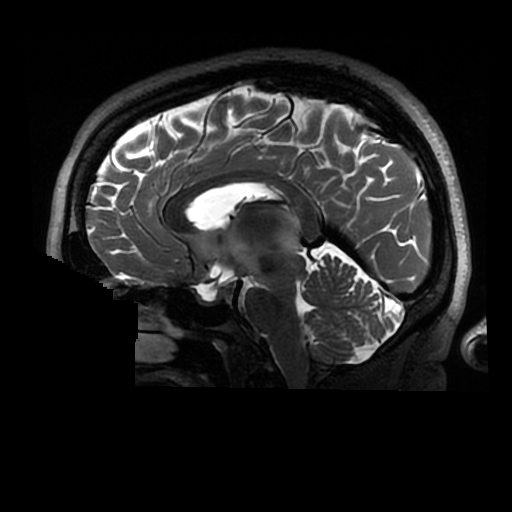
Brain MRI from a brain-tumour surgery series, one sagittal slice; position 154 of 320 along the scan axis; 0.6 mm slice thickness; 512 × 512 image matrix, field of view 240 × 240 mm. From the clinical record (not read from this slice): histopathology: Astrocytoma; WHO grade: 2; IDH mutation: yes.
Structures marked on this image (outlined manually by an expert reader):
- tumour: bounding box (x1, y1, x2, y2) in pixels: (276, 209, 298, 256)